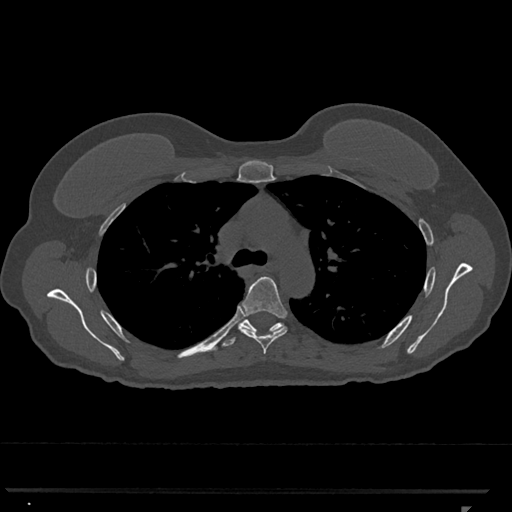
CT including the spine, one axial slice; slice 793 of 793 in the series (ordered by position); reconstruction kernel Br40s/3; 120 kVp; bone window (W 1800 / L 400 HU); 0.5 mm slice thickness; 512 × 512 image matrix, field of view 380 × 380 mm. Patient: female, 62 years. From the clinical record (not read from this slice): primary cancer: renal.
Structures marked on this image (semi-automatically segmented with operator editing):
- T5 vertebra: bounding box <239,277,288,355> (left, top, right, bottom; pixels)
- T6 vertebra: <221,315,283,349>